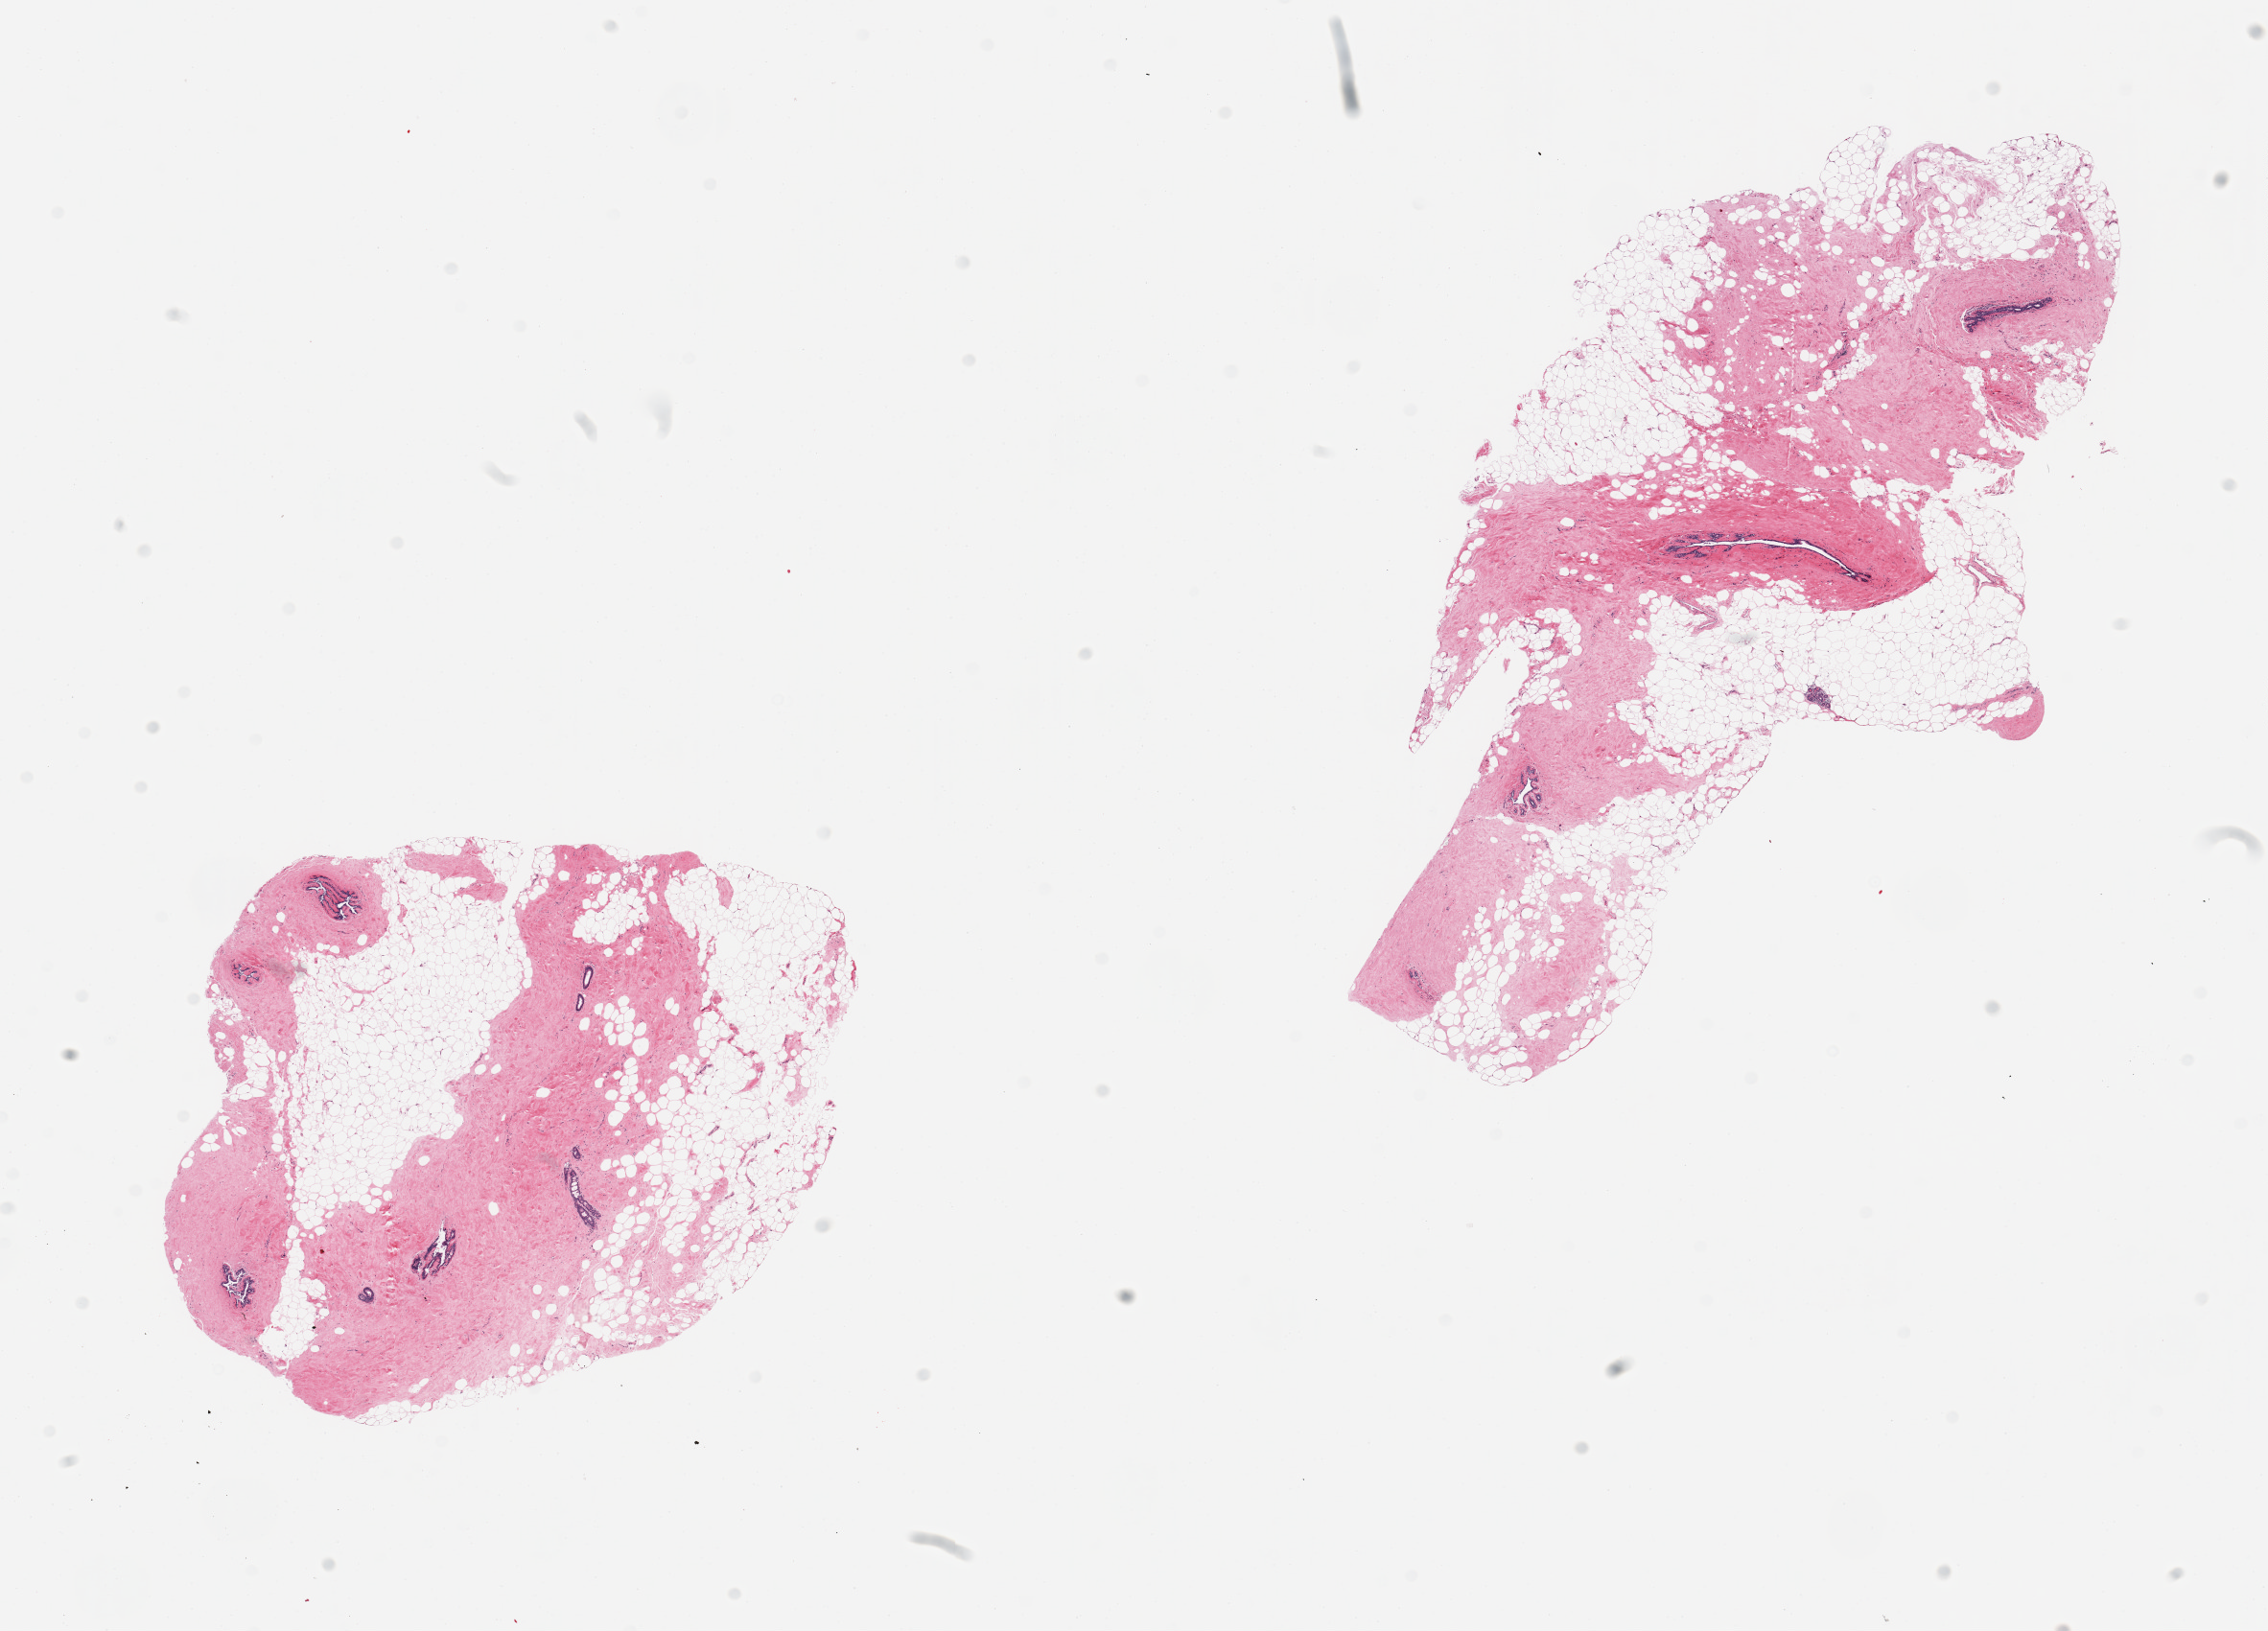
Whole-slide image, H&E stain, whole scanned area (about 18.7 x 13.5 mm) shown as a low-resolution overview. PAXgene-fixed paraffin-embedded (PFPE) section. Target tissue: breast. Tissue donor sample. Donor sex: female.
Review note (as recorded): 2 pieces; atrophic ductal & lobular units; 50% fat.